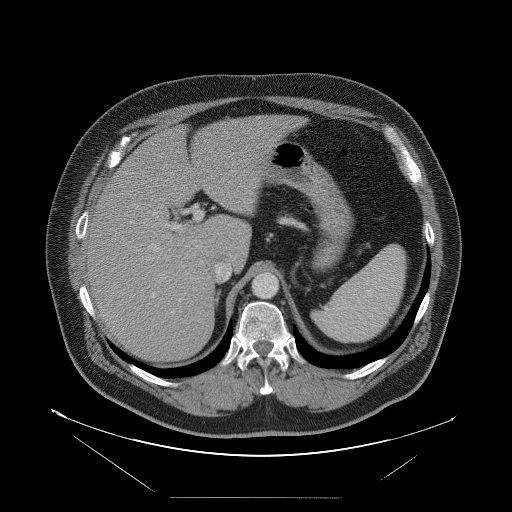
Contrast-enhanced abdominal CT, one axial slice; slice 66 of 114 in the series (ordered by position); 120 kVp; intravenous contrast given; soft-tissue window (W 400 / L 40 HU); 5 mm slice thickness; 512 × 512 image matrix, field of view 500 × 500 mm. Male patient, age 61 years. Case-level facts recorded for this patient, not image findings: diagnosis: colorectal cancer liver metastases, imaged before liver resection; multiple liver metastases: no; largest metastasis: 6.5 cm; disease in both lobes: yes.
Annotated regions visible in this slice (manually delineated by an expert):
- hepatic veins: bounding box [x1, y1, x2, y2] px = [149, 244, 231, 283]
- liver: [88, 115, 294, 362]
- planned liver remnant (the part of the liver to remain after resection): [145, 115, 294, 262]
- portal vein (with intrahepatic branches): [151, 210, 203, 298]